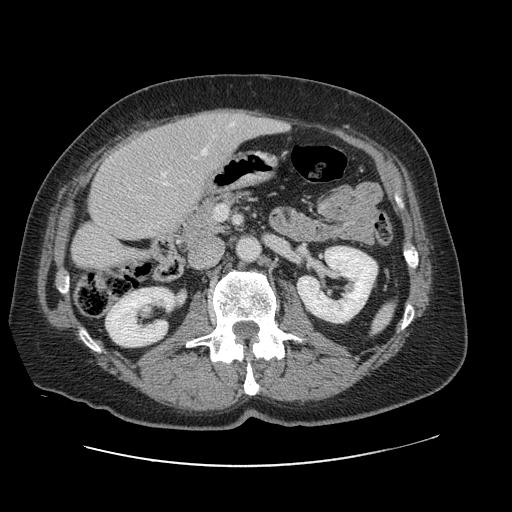
Contrast-enhanced abdominal CT, one axial slice. Position 37 of 138 along the scan axis. Intravenous contrast given. Soft-tissue window (W 400 / L 40 HU). 2.5 mm slice thickness. 512 × 512 image matrix, field of view 402 × 402 mm. Male patient, age 71 years. From the clinical record (not read from this slice): diagnosis: colorectal cancer liver metastases, imaged before liver resection; multiple liver metastases: no; largest metastasis: 3.3 cm; chemotherapy before resection: no.
Structures marked on this image (manually delineated by an expert):
- hepatic veins: box from (x=164, y=123) to (x=234, y=185) px
- liver: (x=72, y=110)–(x=283, y=269)
- planned liver remnant (the part of the liver to remain after resection): (x=73, y=133)–(x=190, y=269)
- portal vein (with intrahepatic branches): (x=162, y=173)–(x=166, y=177)